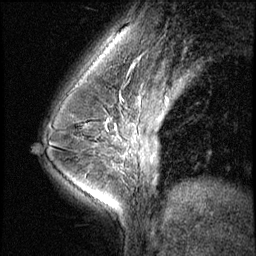
Breast MRI (dynamic contrast-enhanced), one sagittal slice. Position 42 of 60 along the scan axis. 3 images stored at this slice position (order not interpretable as contrast timing). 1.5 T. TE 4.2 ms, TR 8.7 ms. 2.5 mm slice thickness. 256 × 256 image matrix, field of view 180 × 180 mm. Patient: female, 35 years. From the clinical record (not read from this slice): setting: breast cancer imaged before/during neoadjuvant chemotherapy; receptor status: HER2-positive.
Annotated regions visible in this slice (semi-automatically segmented with operator editing):
- analysis volume of interest (the breast-tissue region the enhancement analysis was run in; not a lesion): bounding box <65,102,121,156> (left, top, right, bottom; pixels)
- tumour enhancement mask (voxels above the 140 % enhancement threshold inside the analysis volume of interest): <106,120,108,129>